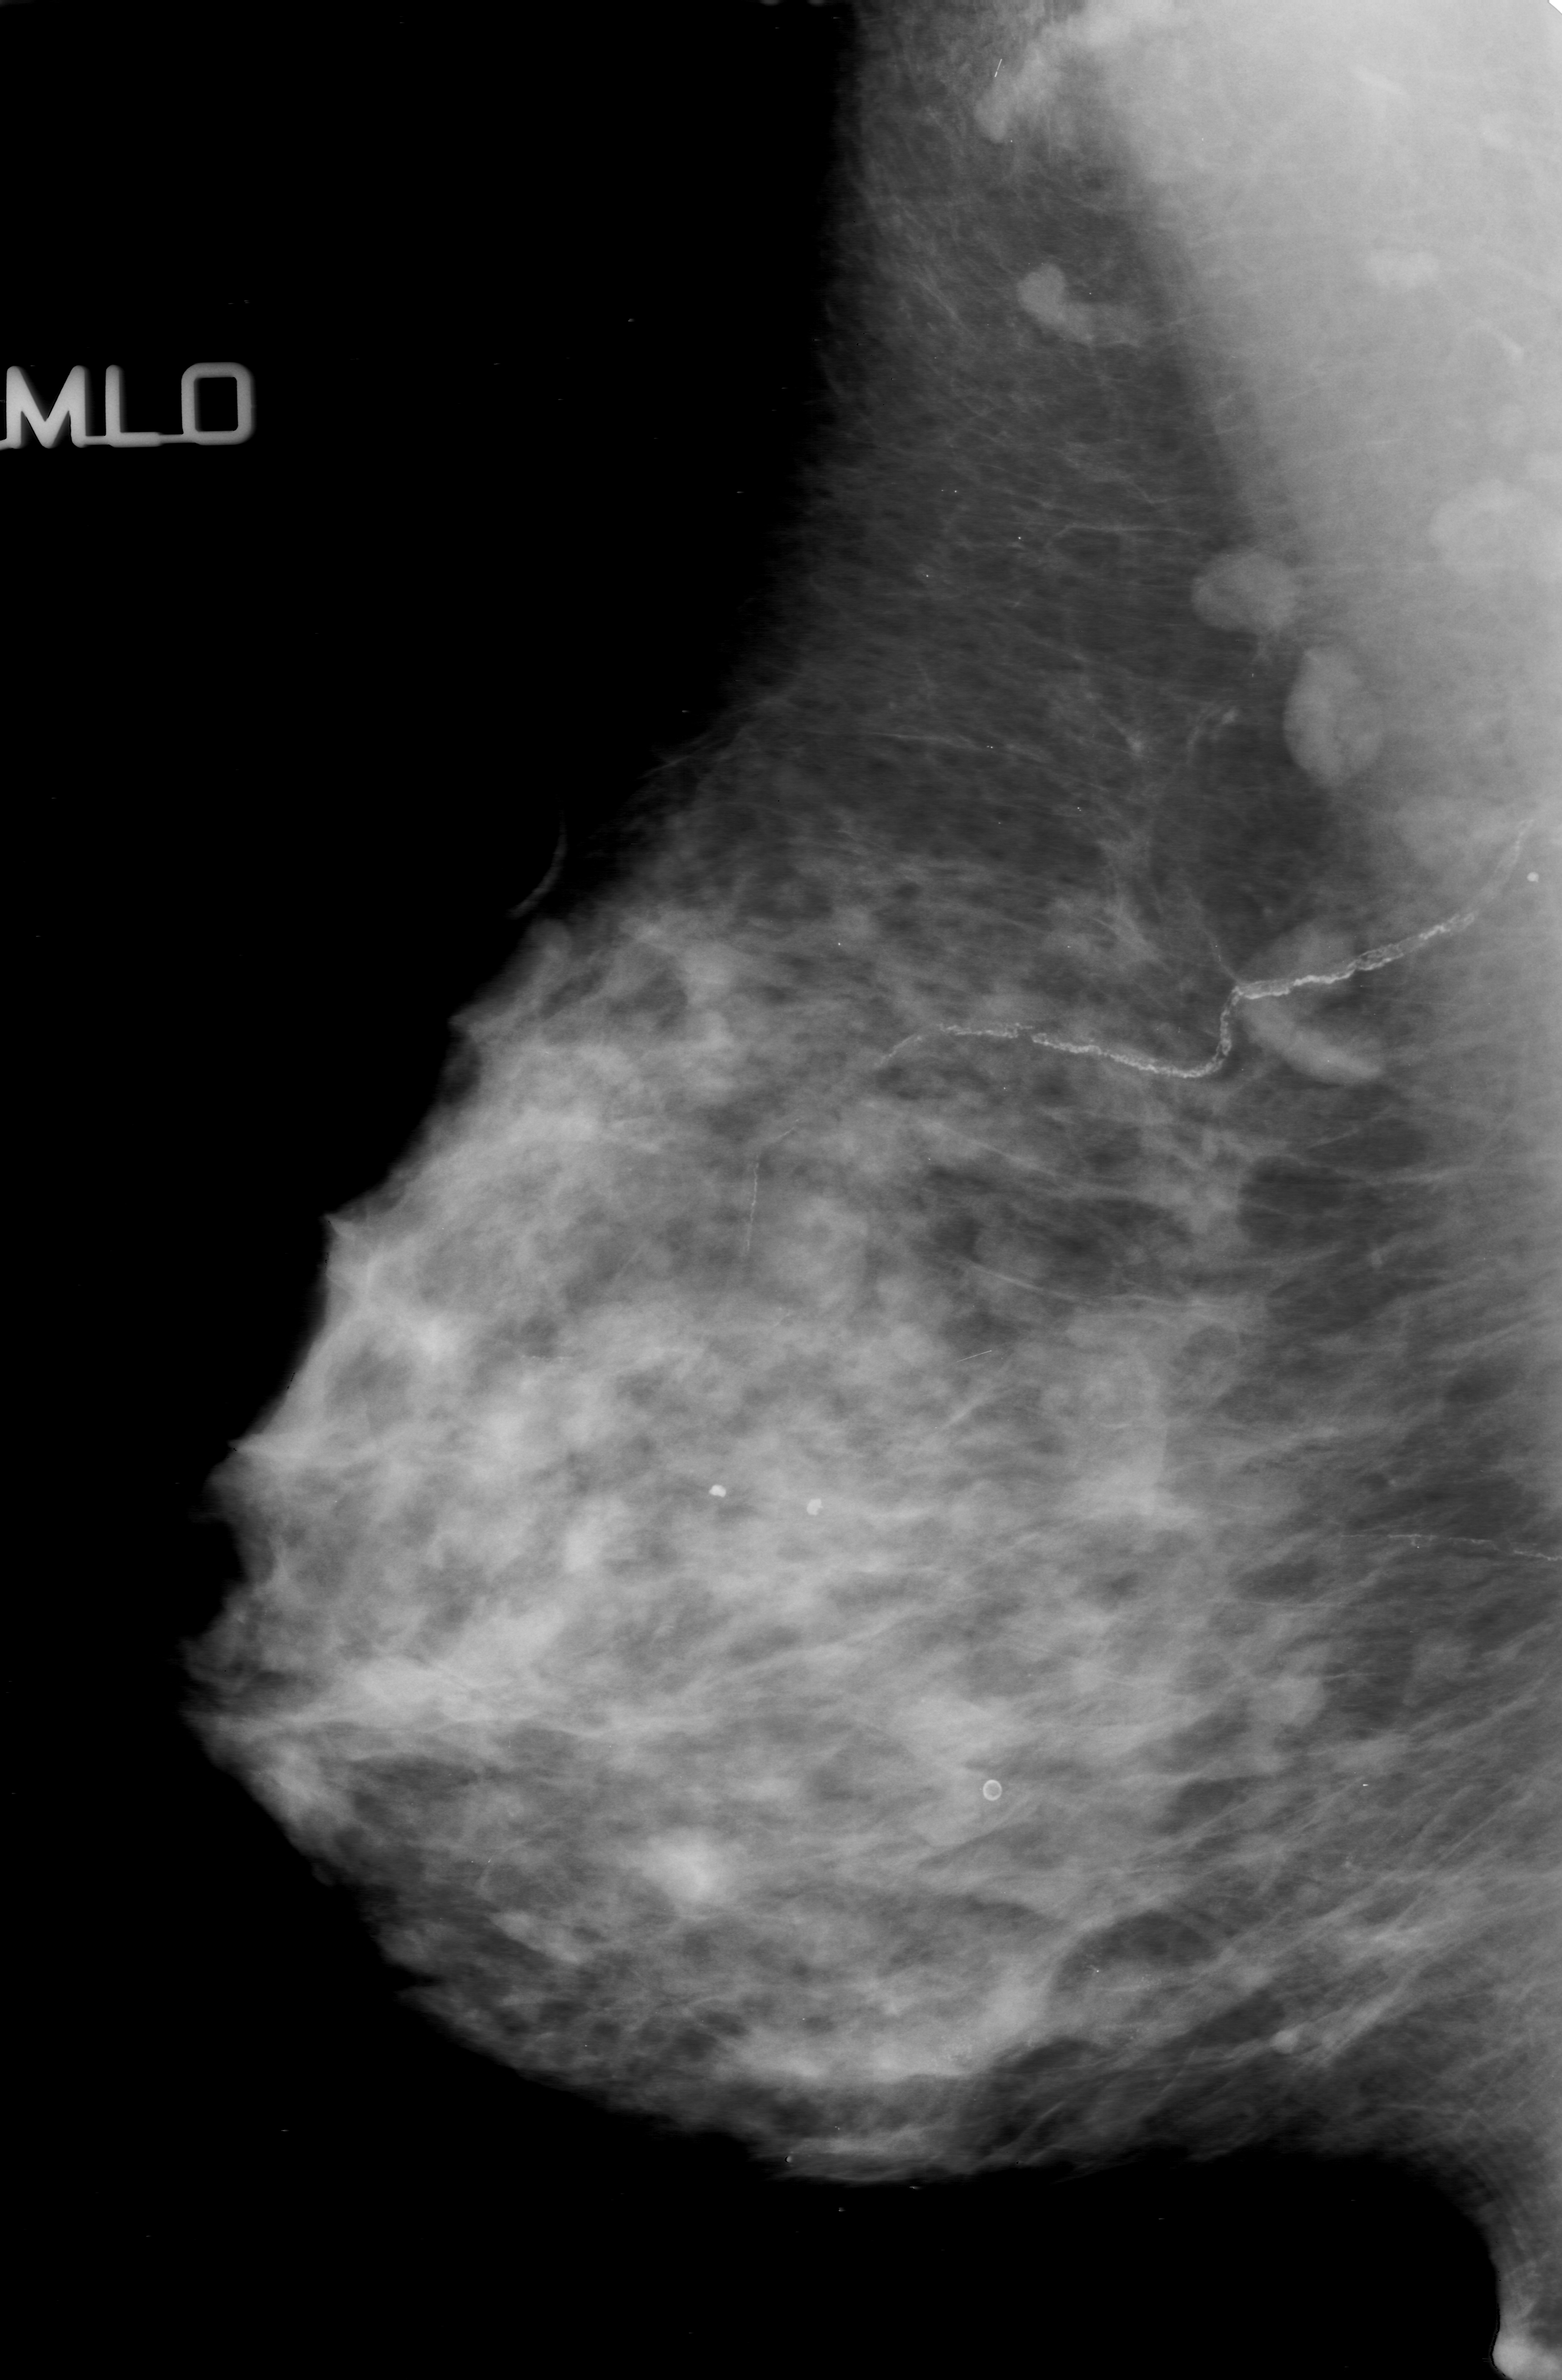
Digitized screen-film mammogram; right breast; MLO view; BI-RADS breast density category 3 (scale 1–4); 1562 × 2380 image matrix.
Expert-marked regions of interest on this film, with their recorded descriptors:
- calcifications, morphology amorphous, distribution segmental; BI-RADS assessment category 5; subtlety rating 3 on a 1 (subtle) to 5 (obvious) scale; pathology result (as recorded, not read from the image): malignant: bounding box [x1, y1, x2, y2] px = [690, 1922, 1303, 2169]